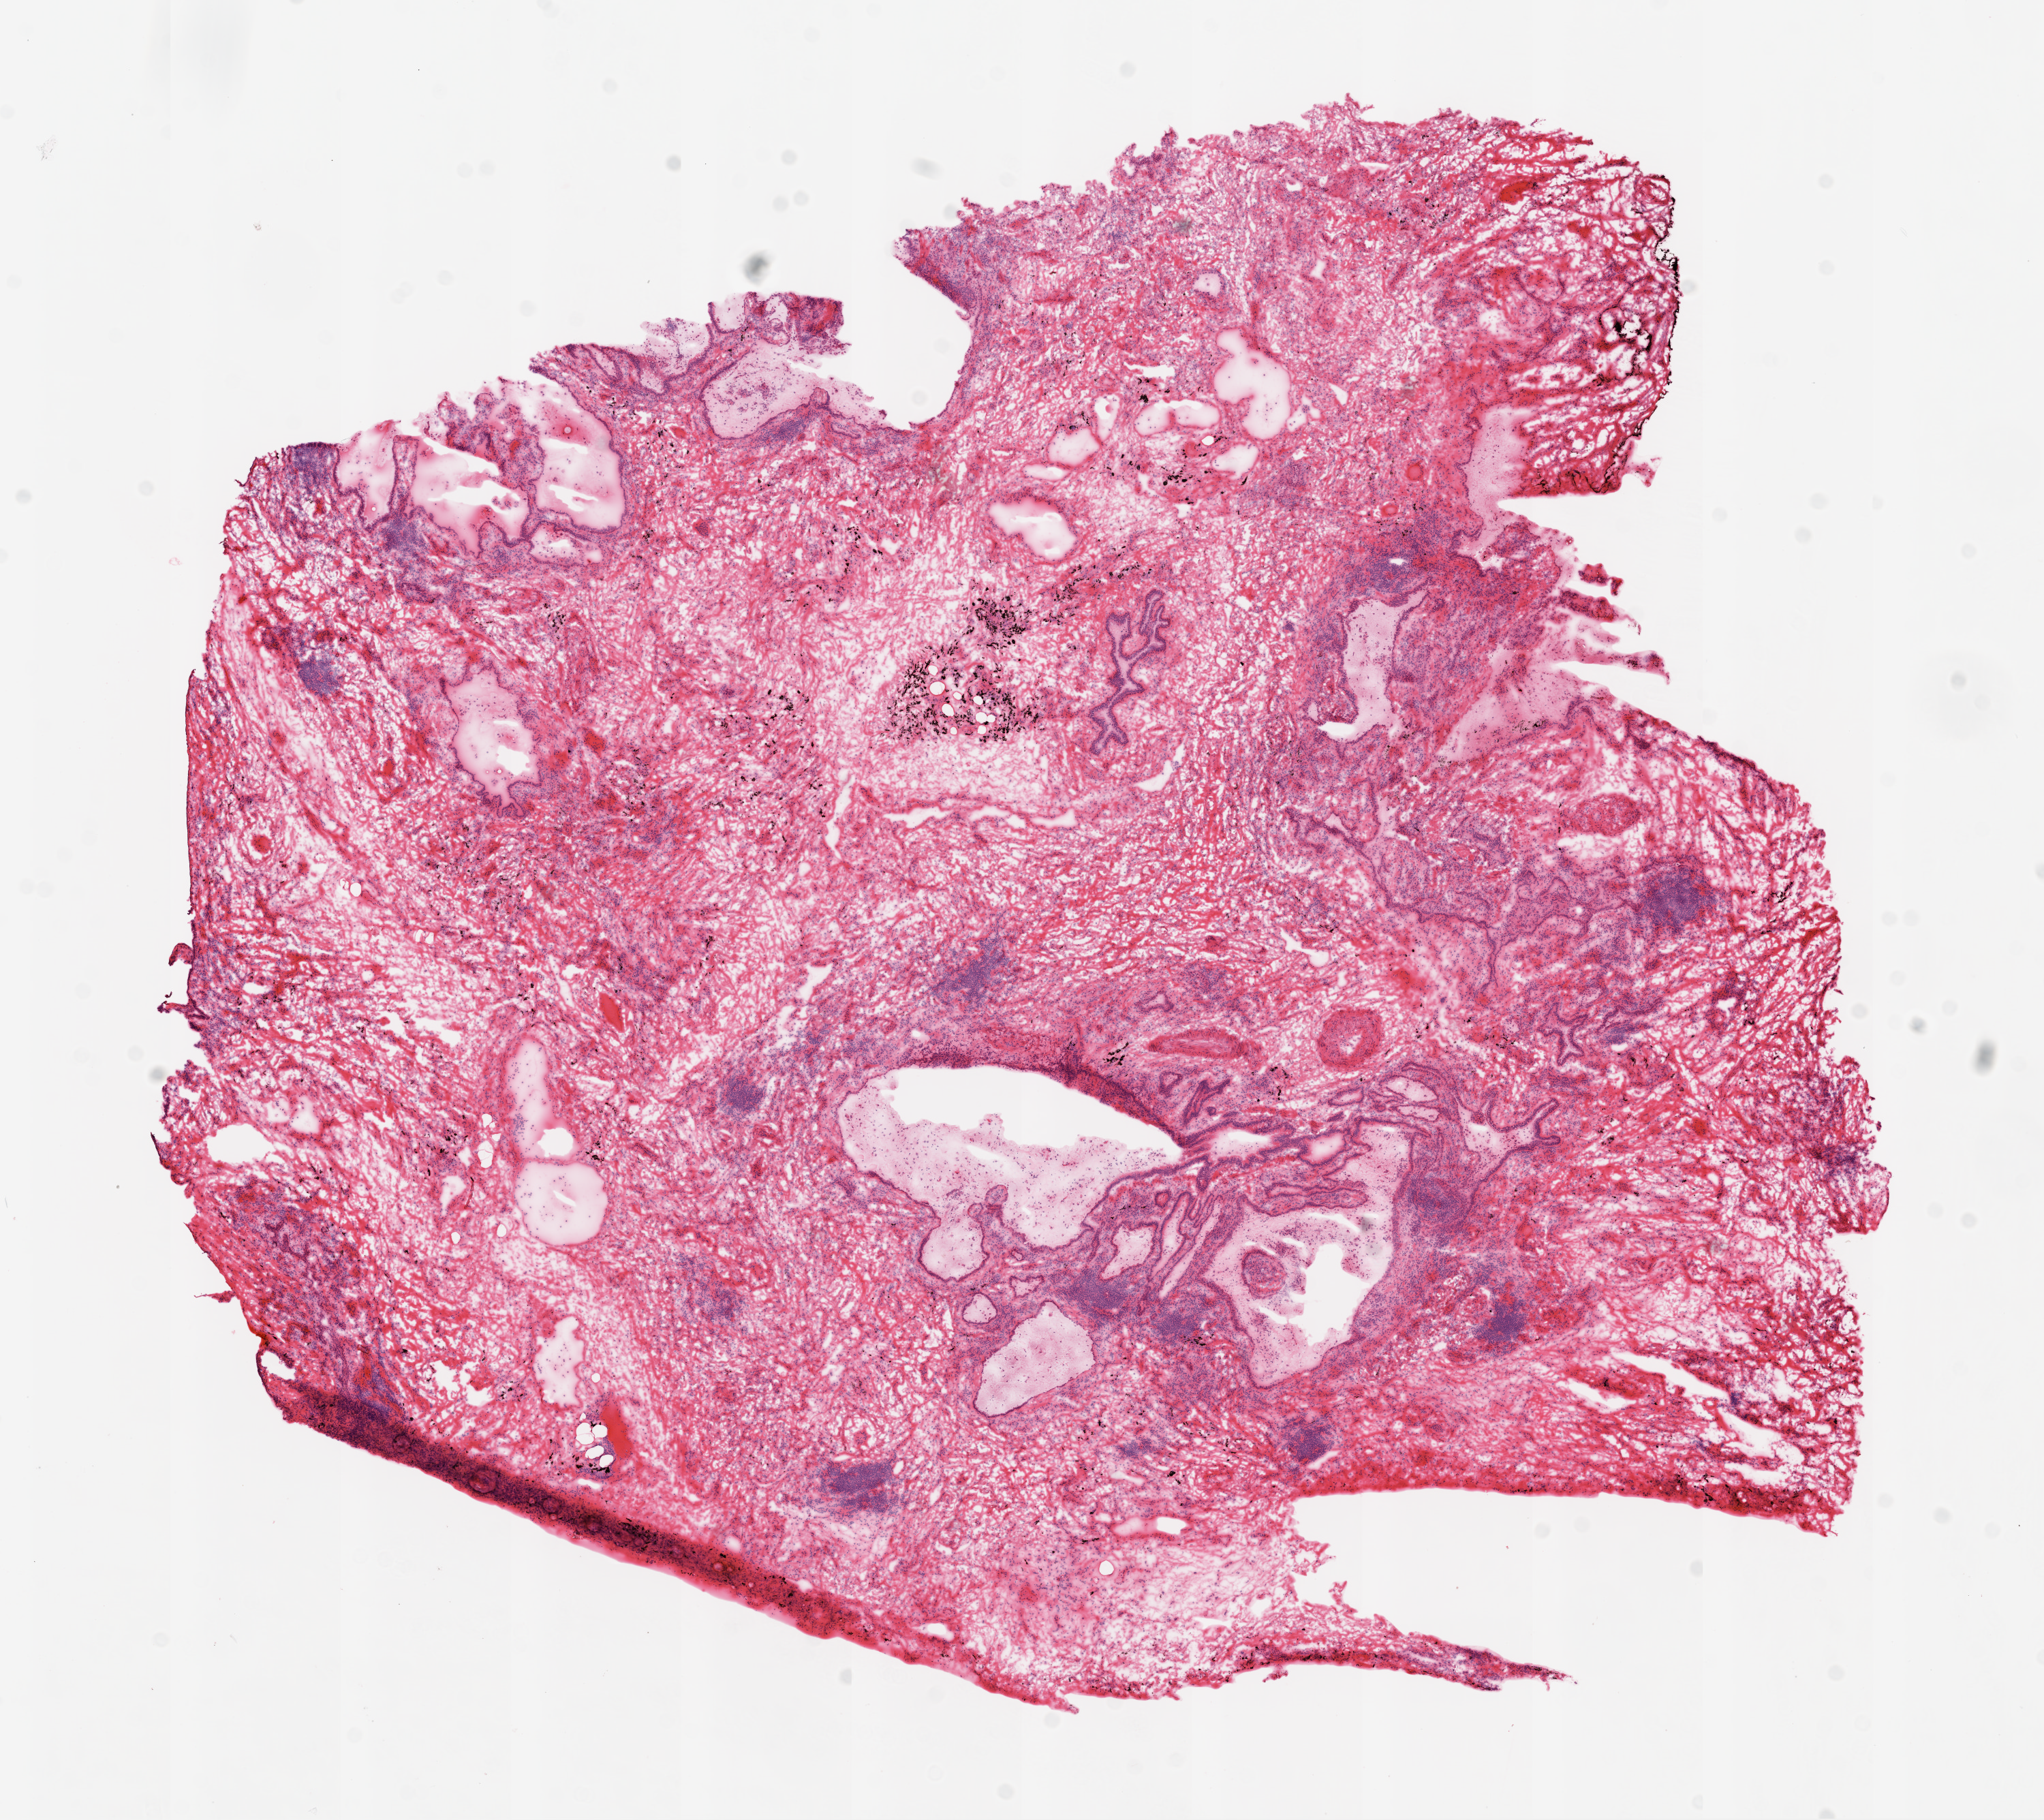
Digitized H&E tissue section (whole slide) — a low-resolution overview of the entire scanned area, about 12.0 x 10.7 mm. Frozen section. Solid tissue normal (non-tumour tissue) sample from the lung. Male patient; age at initial diagnosis 74 years.
* this section: solid tissue normal (non-tumour) sample from the same patient
* patient diagnosis: Squamous cell carcinoma, NOS (upper lobe, lung)